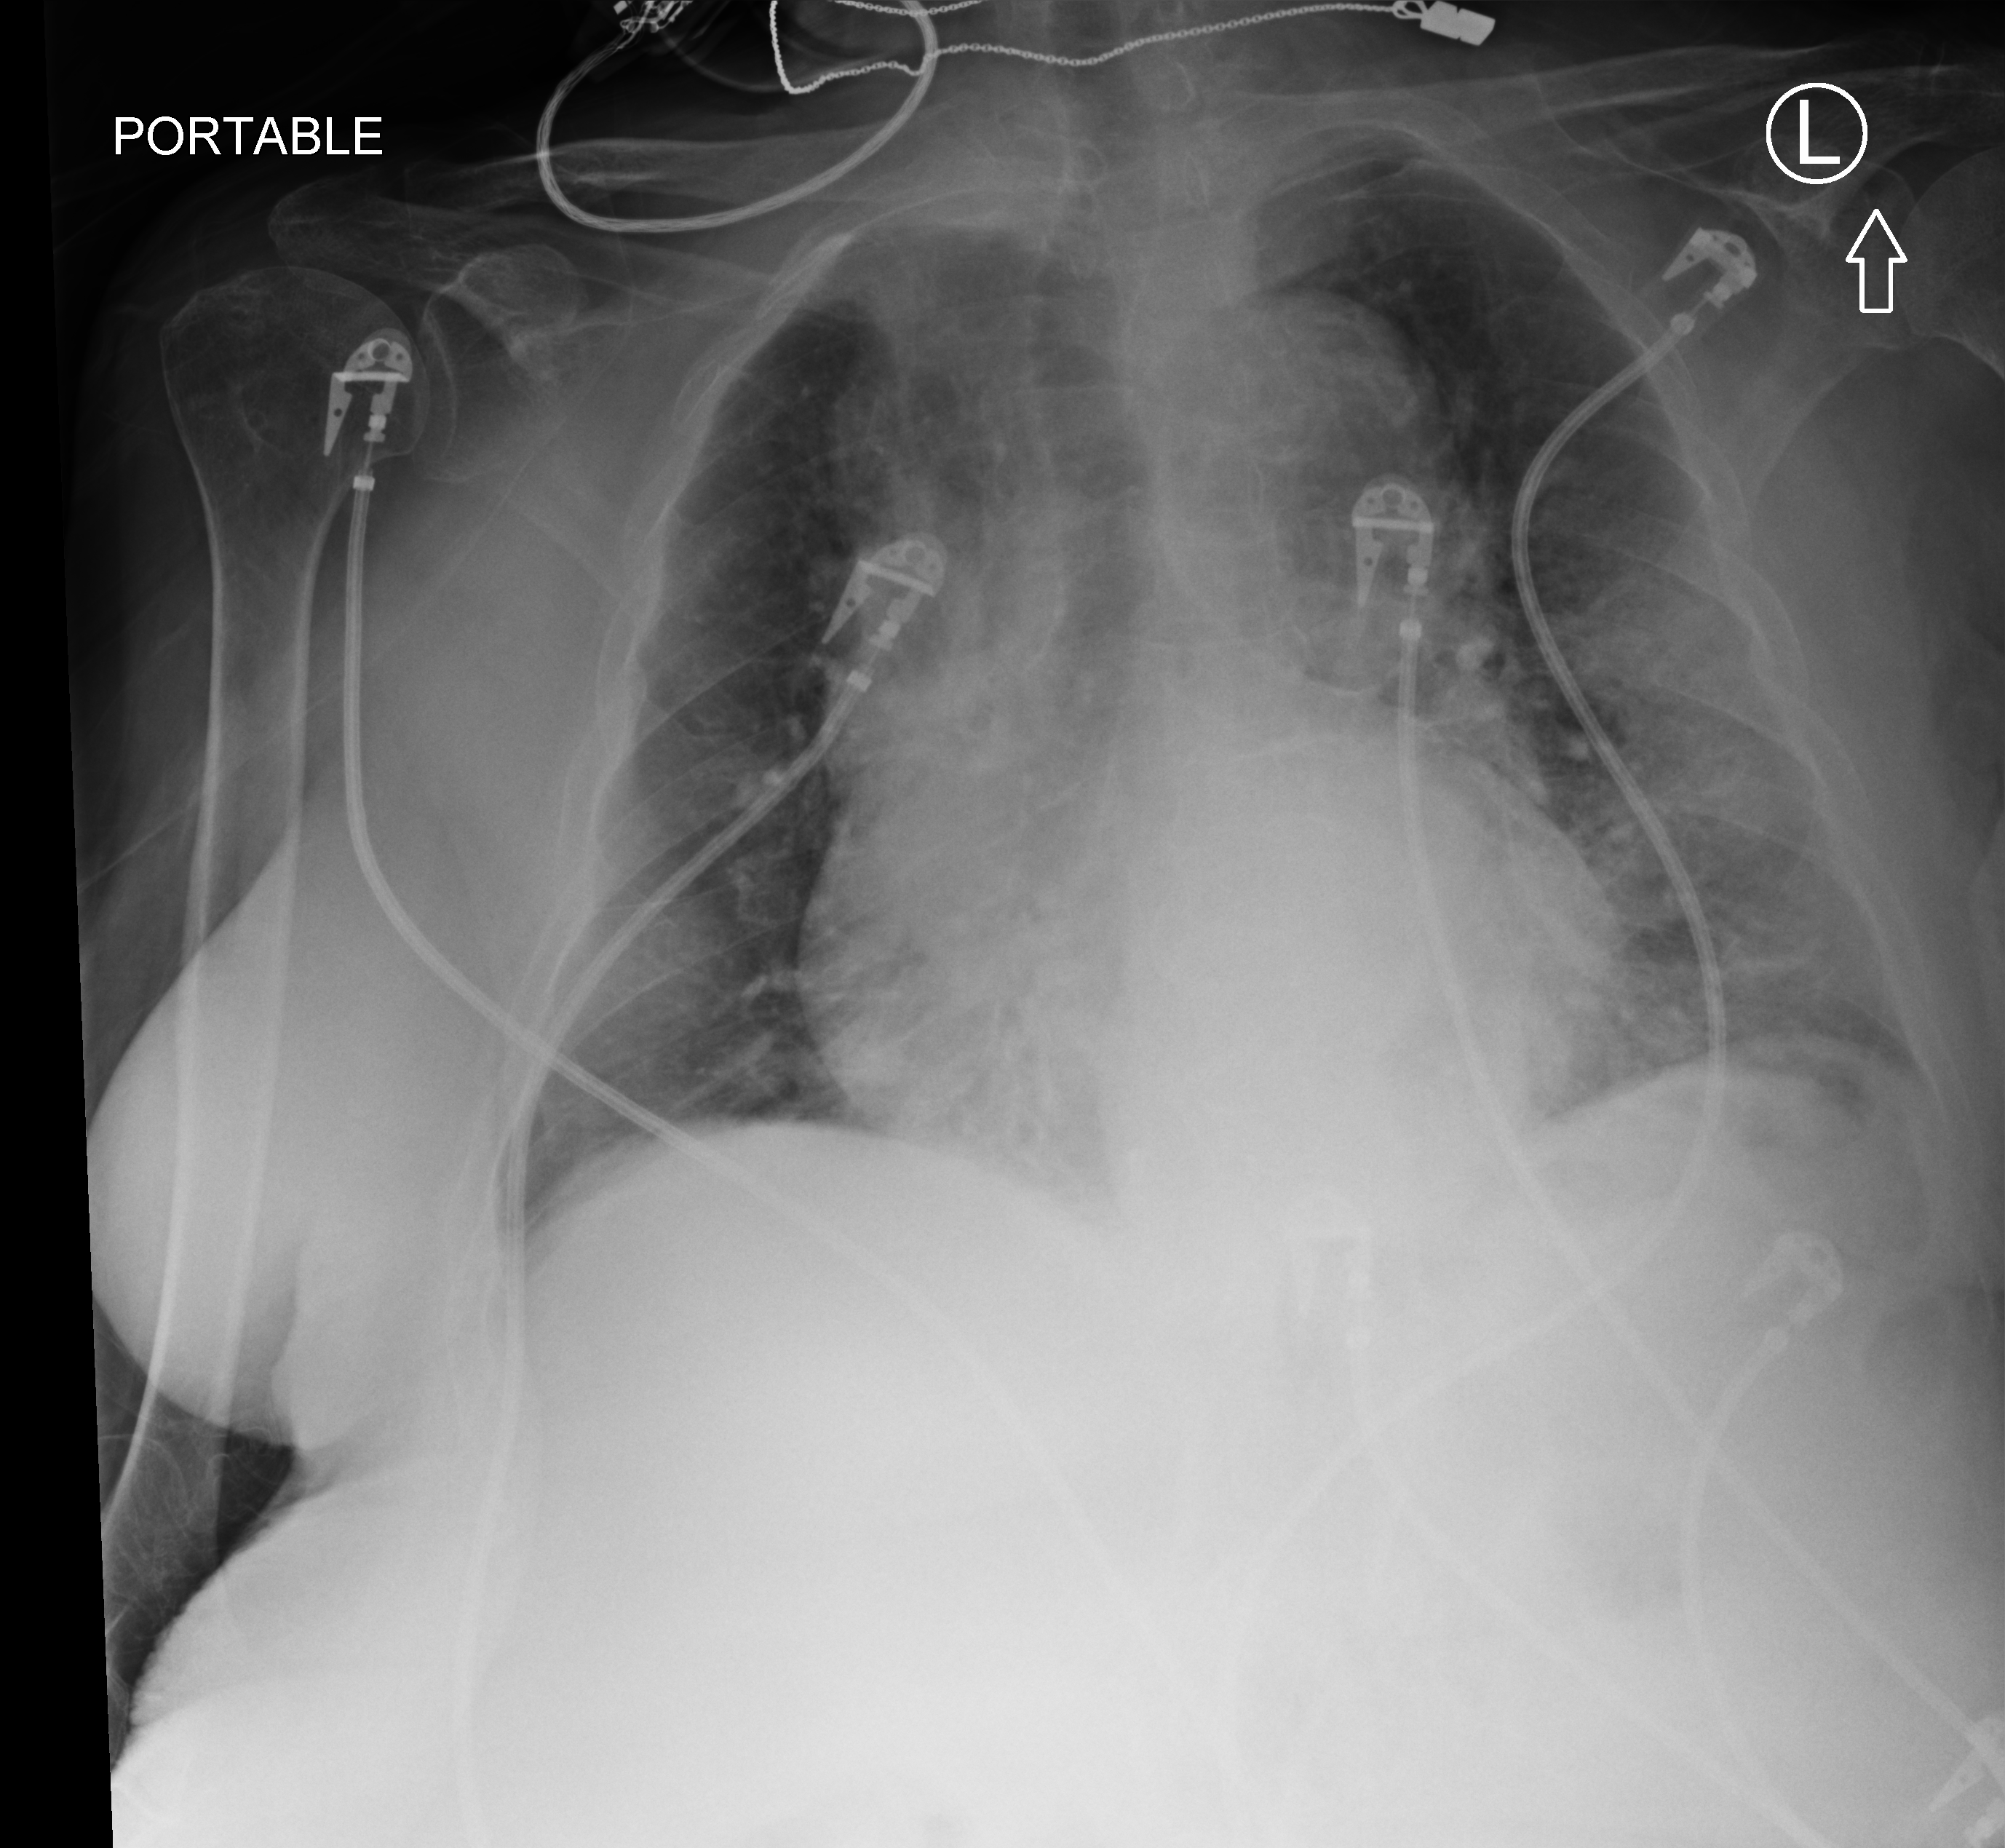
Portable chest radiograph, anteroposterior (AP) projection. Patient hospitalised with COVID-19; female, aged 75–90 years.
Admission-level facts for this patient (not findings on this image; timing relative to this image not recorded):
- mechanically ventilated during this hospital stay: no
- admitted to intensive care during this hospital stay: no